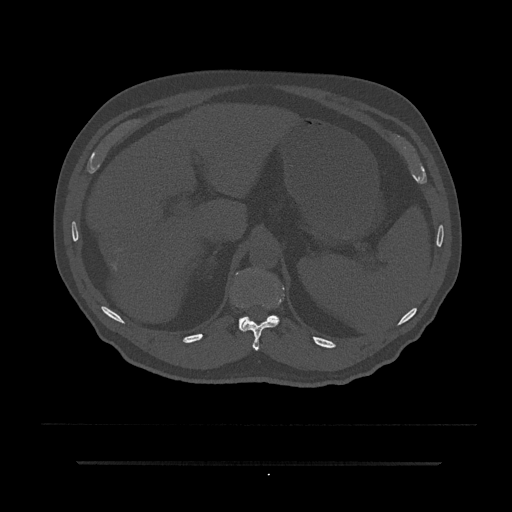
CT including the spine, one axial slice. Position 244 of 797 along the scan axis. Reconstruction kernel Br40s/3. Bone window (W 1800 / L 400 HU). 0.5 mm slice thickness. 512 × 512 image matrix. Patient: male, 59 years. Case-level facts recorded for this patient, not image findings: primary cancer: bile ducts; vertebrae with lytic lesions (as recorded): T10.
Structures marked on this image (semi-automatically segmented with operator editing):
- T11 vertebra: bounding box [x1, y1, x2, y2] px = [242, 300, 282, 351]
- T12 vertebra: [239, 315, 279, 332]